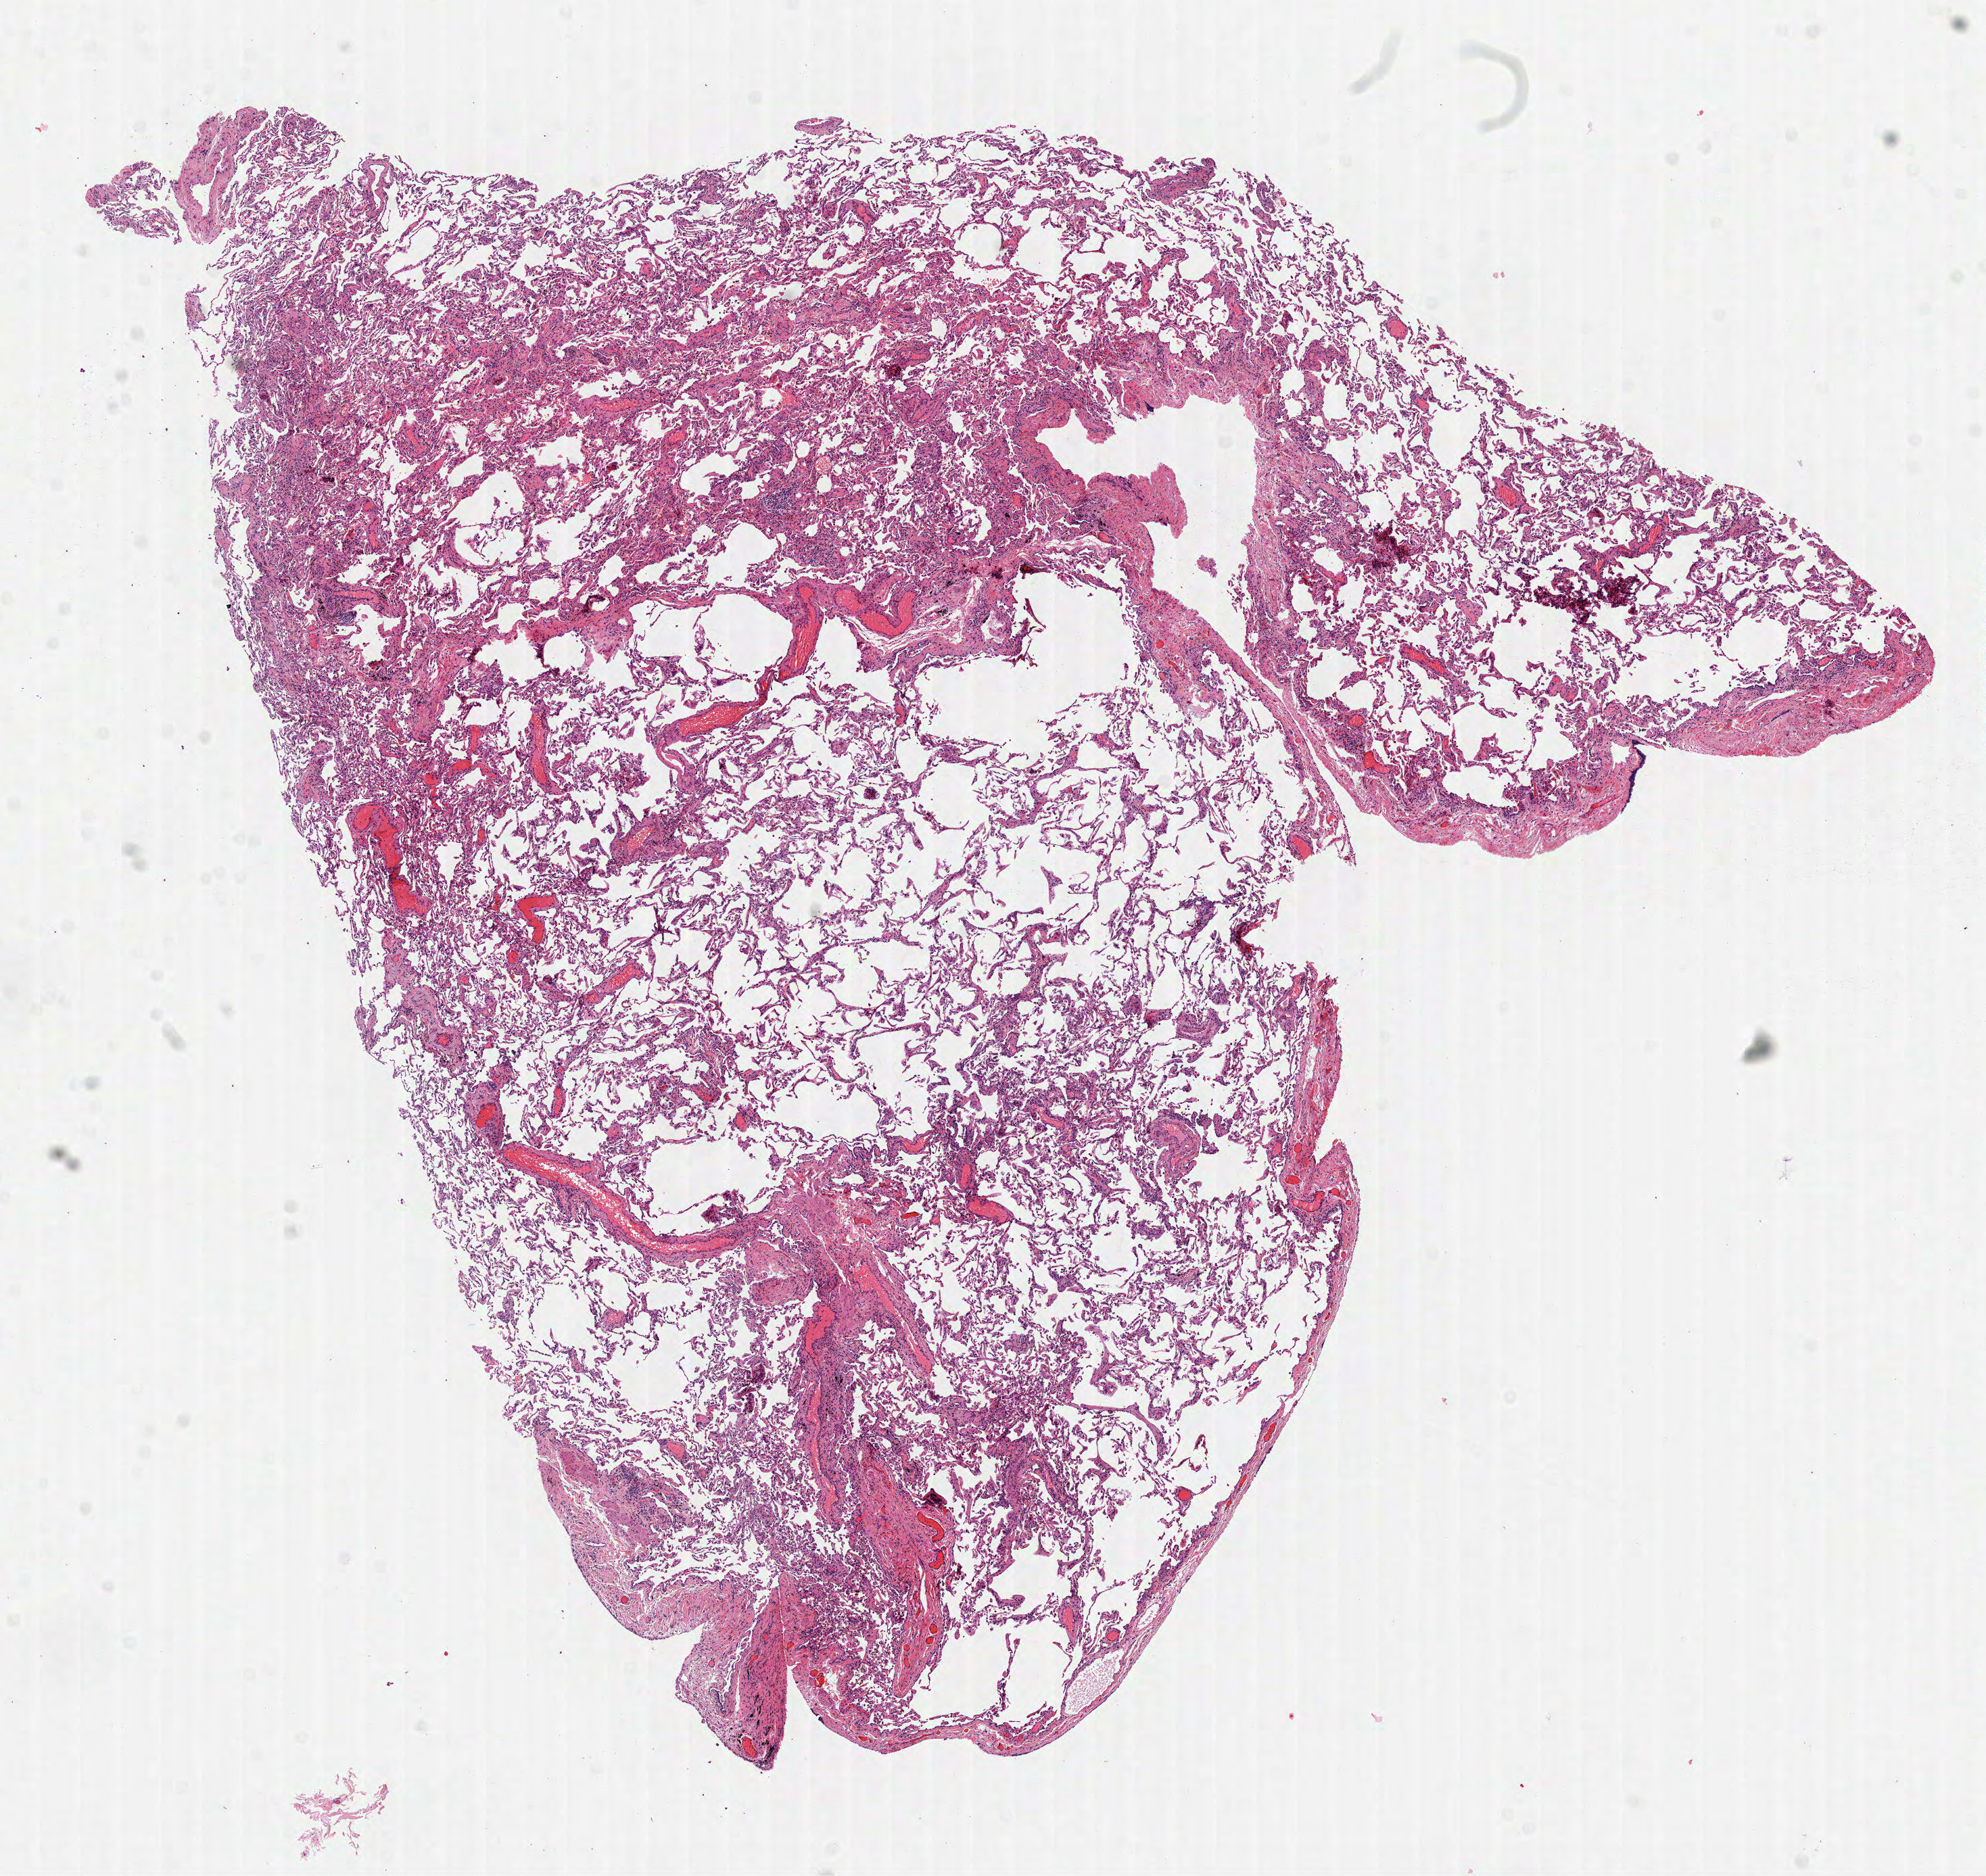
Digitized Hematoxylin and eosin (H&E) stained tissue section (whole slide) — a low-resolution overview of the entire scanned area, about 11.8 x 11.2 mm. Frozen section. Lung, solid tissue normal (non-tumour tissue) sample. Male, age 55 years at initial diagnosis. Inflammatory infiltration, as recorded: lymphocyte infiltration 5%, monocyte infiltration 0%, neutrophil infiltration 30%.
This section: solid tissue normal sample (biorepository sample class). Patient diagnosis: Squamous cell carcinoma, NOS.